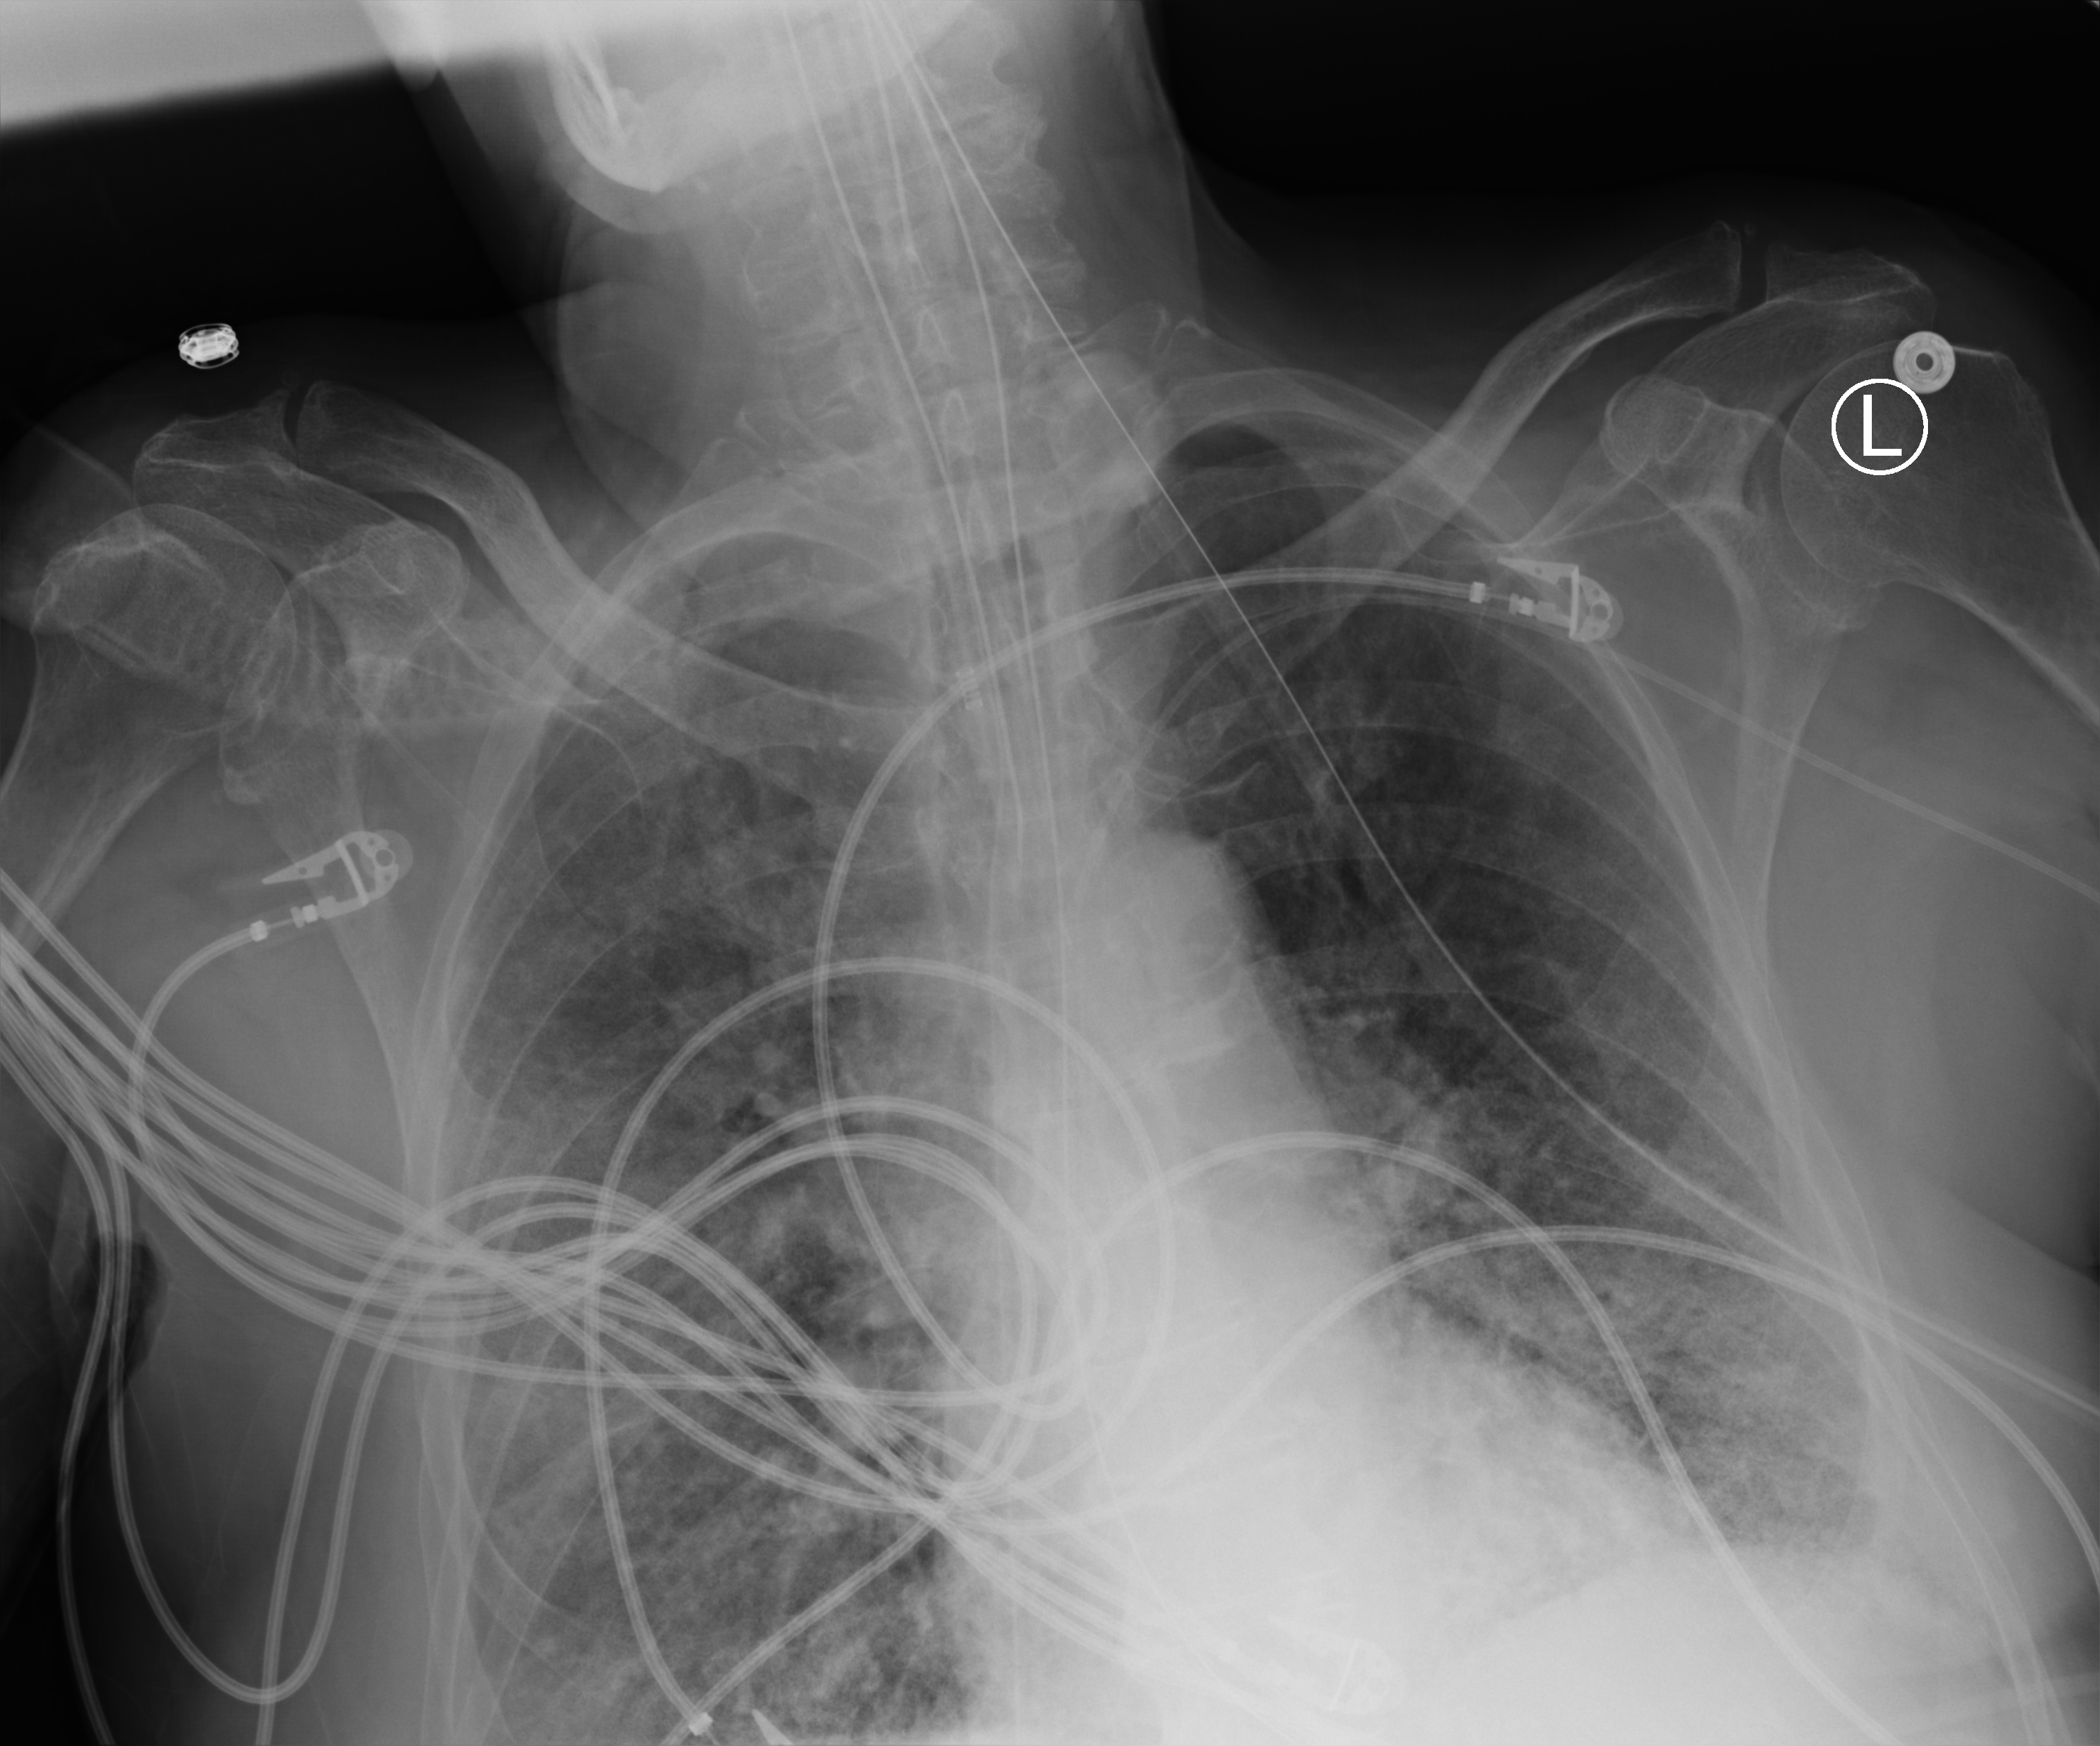
Bedside chest radiograph (computed radiography), anteroposterior (AP) projection. Male patient hospitalised with COVID-19, age 75–90 years.
Hospital-stay facts (about this admission, not read from this image; timing relative to this image not recorded): mechanically ventilated during this hospital stay: yes.